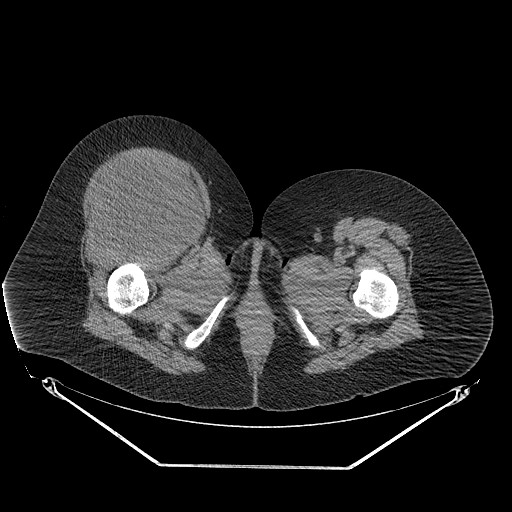
CT of an extremity soft-tissue mass (from a PET/CT study), one axial slice; position 52 of 267 along the scan axis; 140 kVp; soft-tissue window (W 400 / L 40 HU); 3.75 mm slice thickness; 512 × 512 image matrix, field of view 500 × 500 mm. Female patient. From the clinical record (not read from this slice): histological type: malignant solitary fibrous tumor; grade: intermediate; site of the primary tumour: right thigh.
Outlined on this slice (expert contour drawn on MRI and transferred to this co-registered scan by the dataset authors):
- gross tumour volume including surrounding oedema: box from (x=78, y=155) to (x=202, y=245) px
- gross tumour volume (mass): (x=78, y=157)–(x=197, y=243)